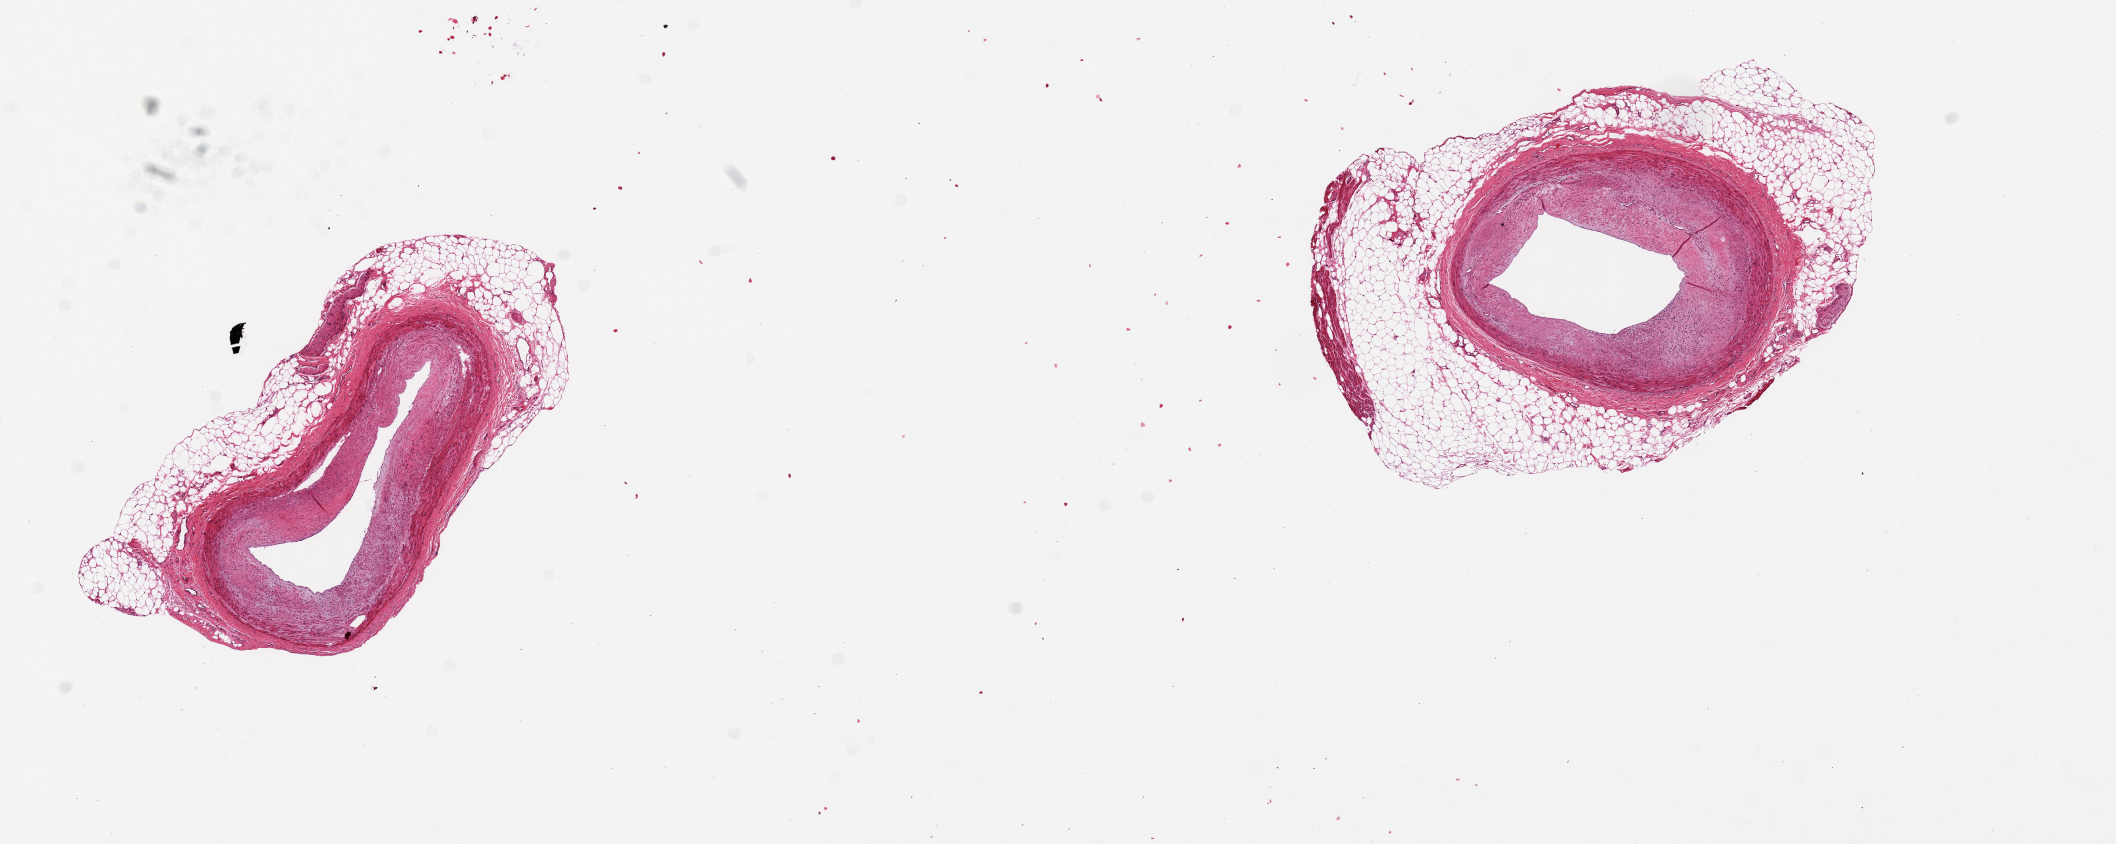
Digitized haematoxylin and eosin-stained section, brightfield, a low-resolution overview of the entire scanned area, about 16.7 x 6.7 mm (slide scanned at 20x), PAXgene-fixed, paraffin-embedded tissue, target tissue: coronary artery, tissue donor sample. Male donor.
- review note (as recorded): 2 pieces, 2.9 mm diameter; 40% atherosclerotic occlusion